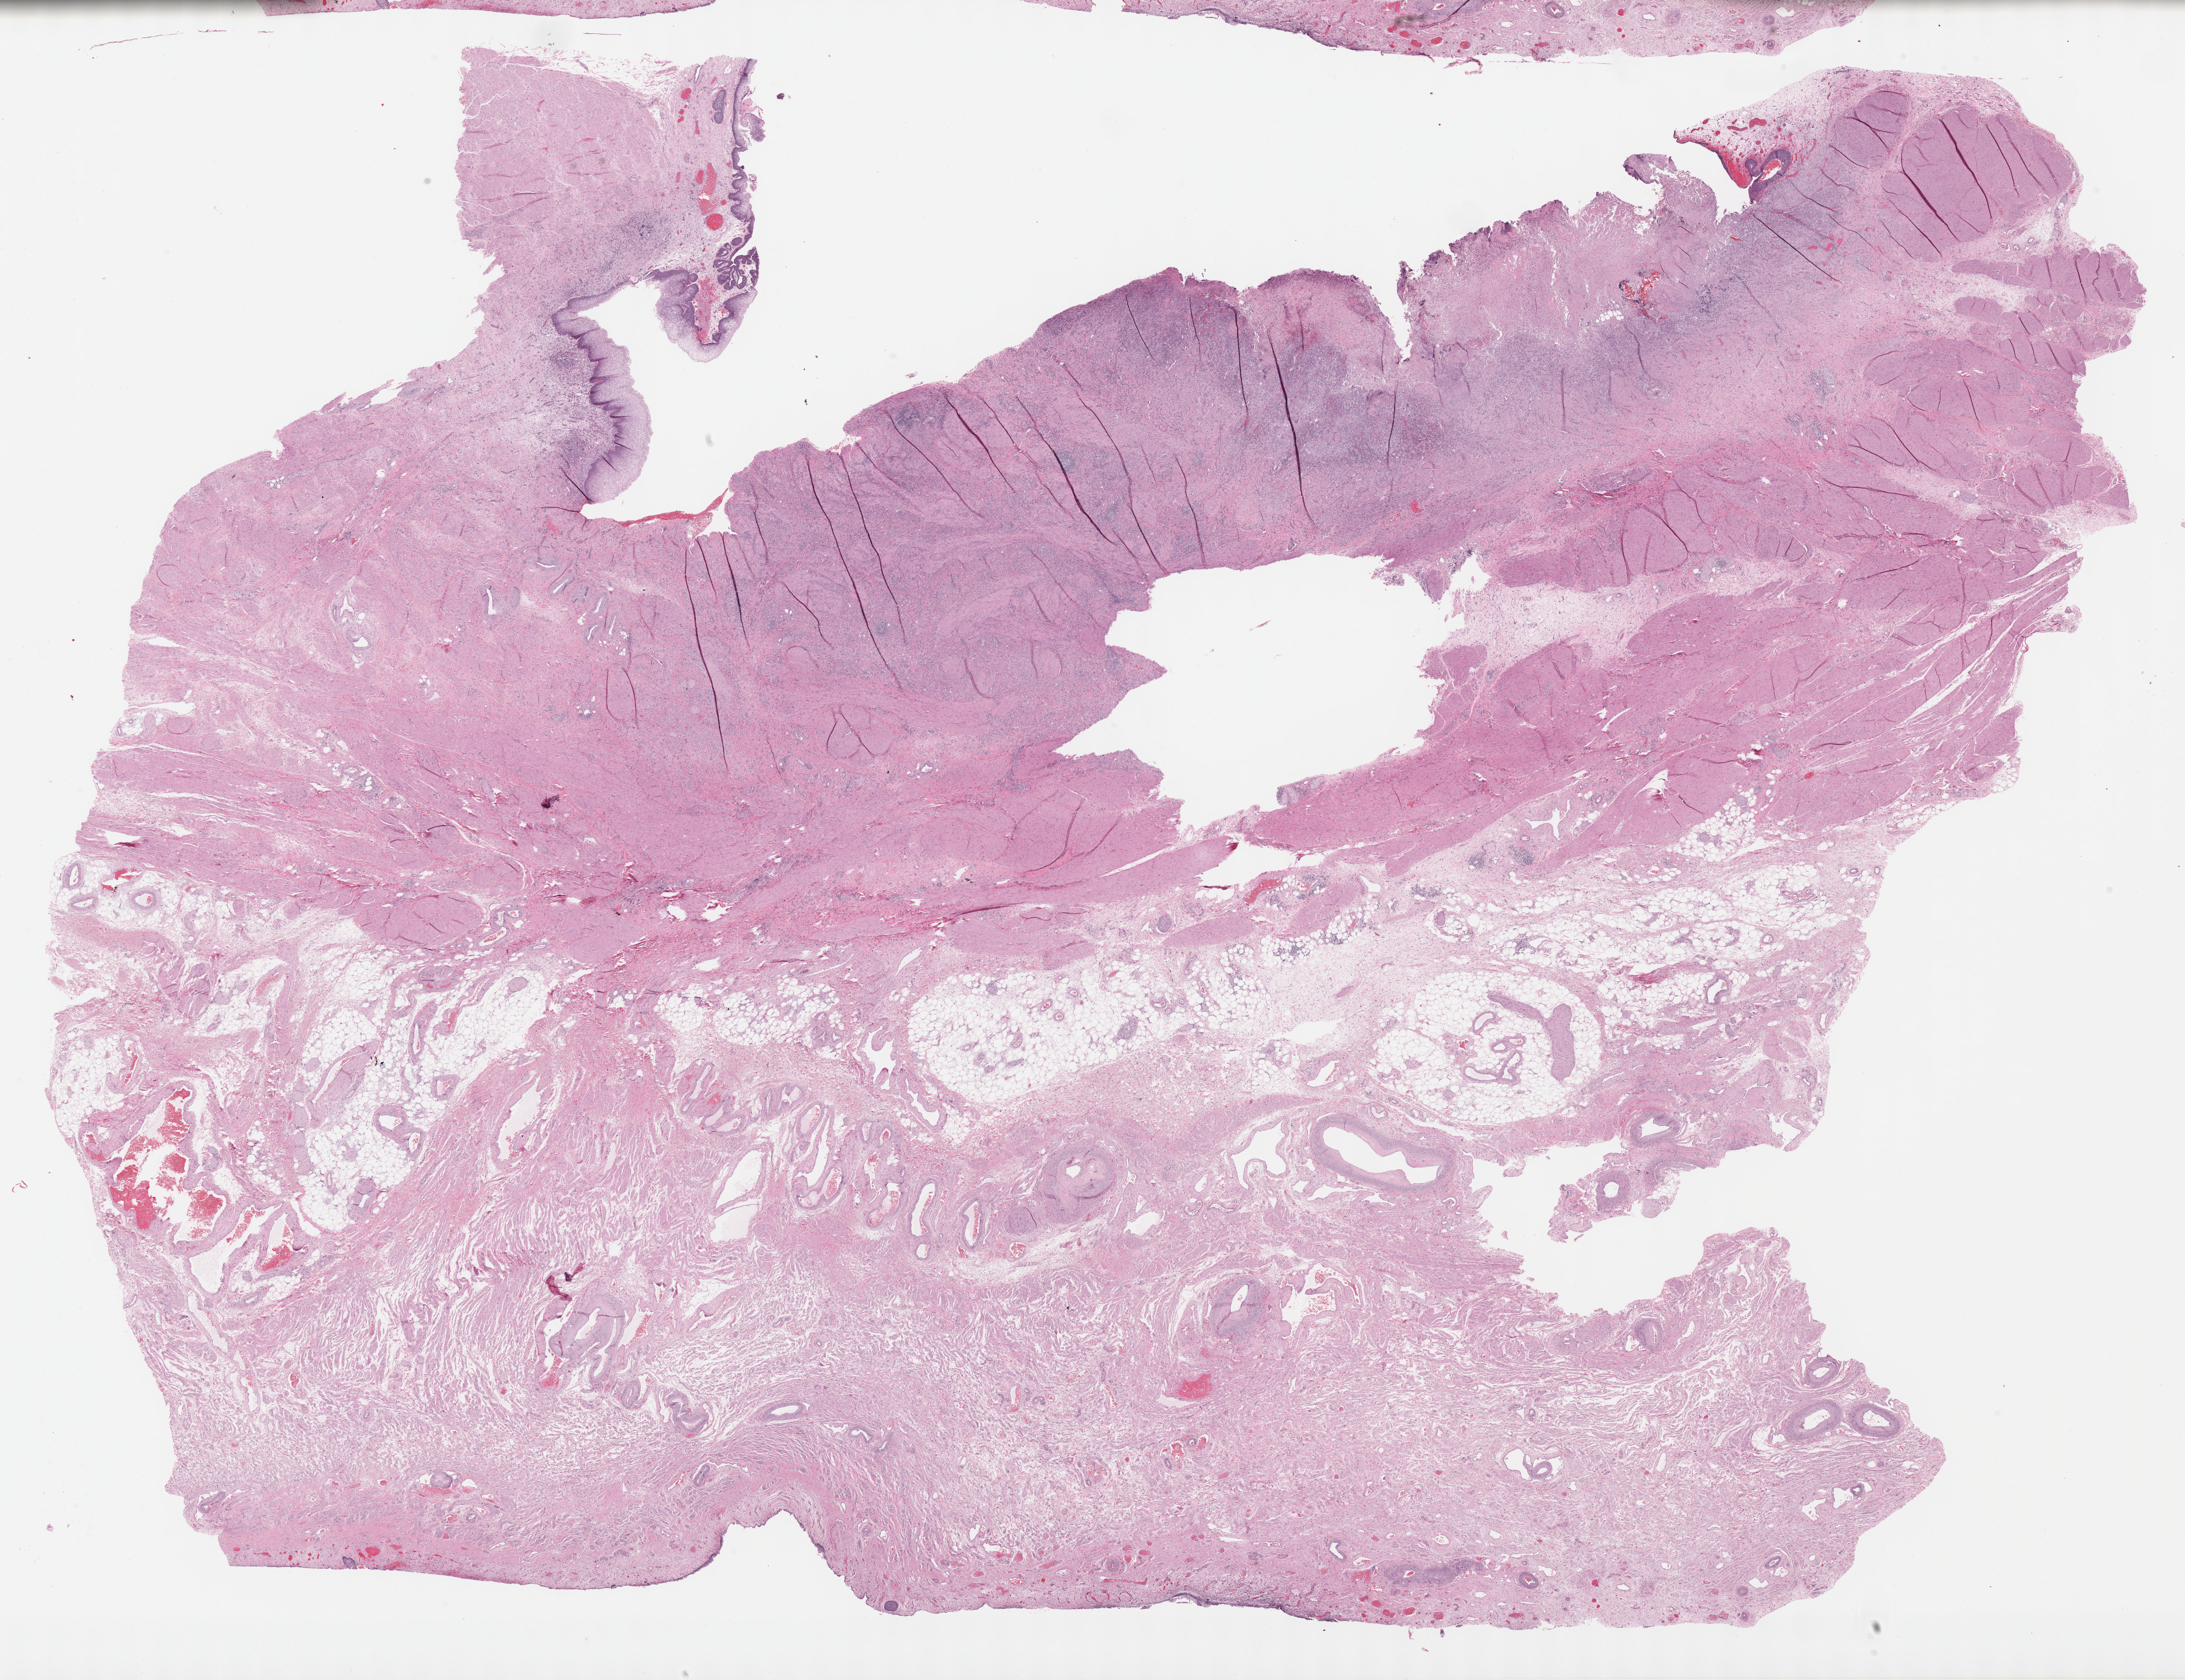
H&E whole-slide image — a low-resolution overview of the entire scanned area, about 30.2 x 23.2 mm (from a 40x scan). Formalin-fixed paraffin-embedded (FFPE) diagnostic section. Bladder, primary tumour sample. Female patient; age at initial diagnosis 84 years. Histologic grade: high grade.
Lymph nodes positive (case pathology): 4 of 14 examined. AJCC pathologic stage: IV (6th edition). Histologic diagnosis: Transitional cell carcinoma.